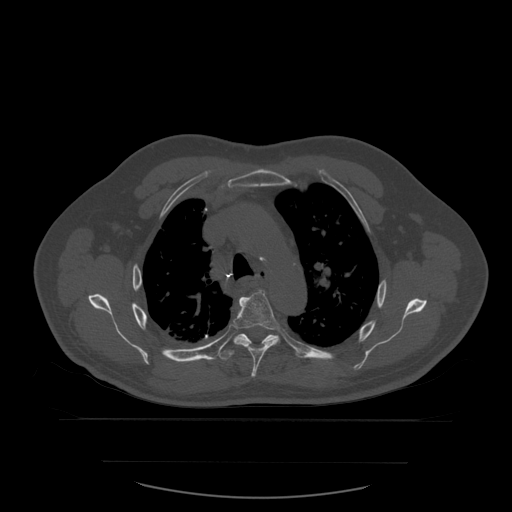
CT including the spine, one axial slice; slice 419 of 590 in the series (ordered by position); bone window (W 1800 / L 400 HU); 1.25 mm slice thickness; 512 × 512 image matrix, field of view 479 × 479 mm. Patient age 71 years. From the clinical record (not read from this slice): primary cancer: lung; vertebrae with lytic lesions (as recorded): T1, T2, L5, S1.
Structures marked on this image (semi-automatic segmentation, software-assisted and operator-edited):
- T5 vertebra: bounding box (x1, y1, x2, y2) in pixels: (233, 290, 280, 378)
- T6 vertebra: (222, 334, 279, 361)